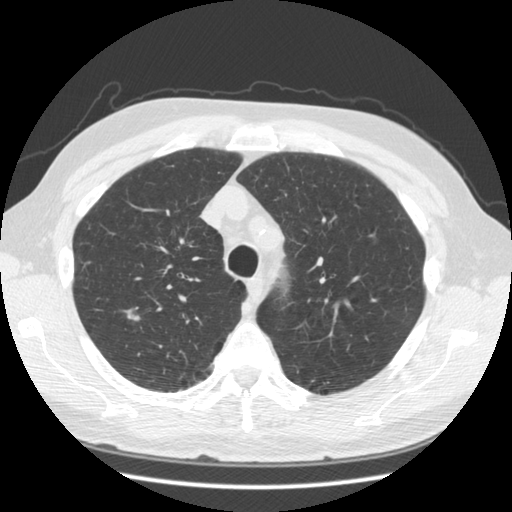
Axial slice from a low-dose chest CT screening exam, second screening round (one year after baseline), lung window (W 1500 / L -600 HU), standard (soft-tissue) reconstruction kernel (STANDARD). Male, age 68 years at enrolment. Current smoker at enrolment.
Expert reader's lesion annotation, bounding box (x1, y1, x2, y2) in pixels: (105, 296, 157, 340). Screening reader's record for this exam: no non-calcified nodule ≥4 mm recorded. Lung cancer was diagnosed 596 days after this screen: adenocarcinoma, NOS, right upper lobe, moderately differentiated (G2), stage IA (AJCC 6th edition), 13 mm at pathology.